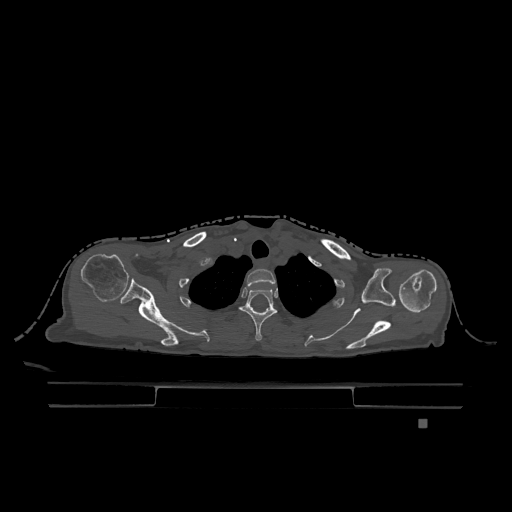
CT including the spine, one axial slice; slice 964 of 1317 in the series (ordered by position); bone window (W 1800 / L 400 HU); 0.5 mm slice thickness; 512 × 512 image matrix, field of view 500 × 500 mm. Patient: female, 74 years. Case-level facts recorded for this patient, not image findings: primary cancer: lung.
Outlined on this slice (semi-automatically segmented with operator editing):
- T1 vertebra: box from (x=246, y=269) to (x=276, y=288) px
- T2 vertebra: (x=239, y=289)–(x=278, y=341)